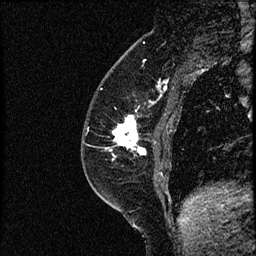
Breast MRI (dynamic contrast-enhanced), one sagittal slice. Position 22 of 52 along the scan axis. Dynamic contrast-enhanced study with each time point stored as its own series, time point 2 of 3 at this slice position (early post-contrast, ordered by acquisition time). 1.5 T. TE 4.2 ms, TR 17.6 ms. 2 mm slice thickness. 256 × 256 image matrix, field of view 200 × 200 mm. Female patient, age 49 years. Case-level facts recorded for this patient, not image findings: setting: breast cancer imaged before/during neoadjuvant chemotherapy; receptor status: HER2-positive.
Structures marked on this image (semi-automatically segmented with operator editing):
- analysis volume of interest (the breast-tissue region the enhancement analysis was run in; not a lesion): bounding box <85,65,182,175> (left, top, right, bottom; pixels)
- tumour enhancement mask (voxels above the 100 % enhancement threshold inside the analysis volume of interest): <114,116,147,155>